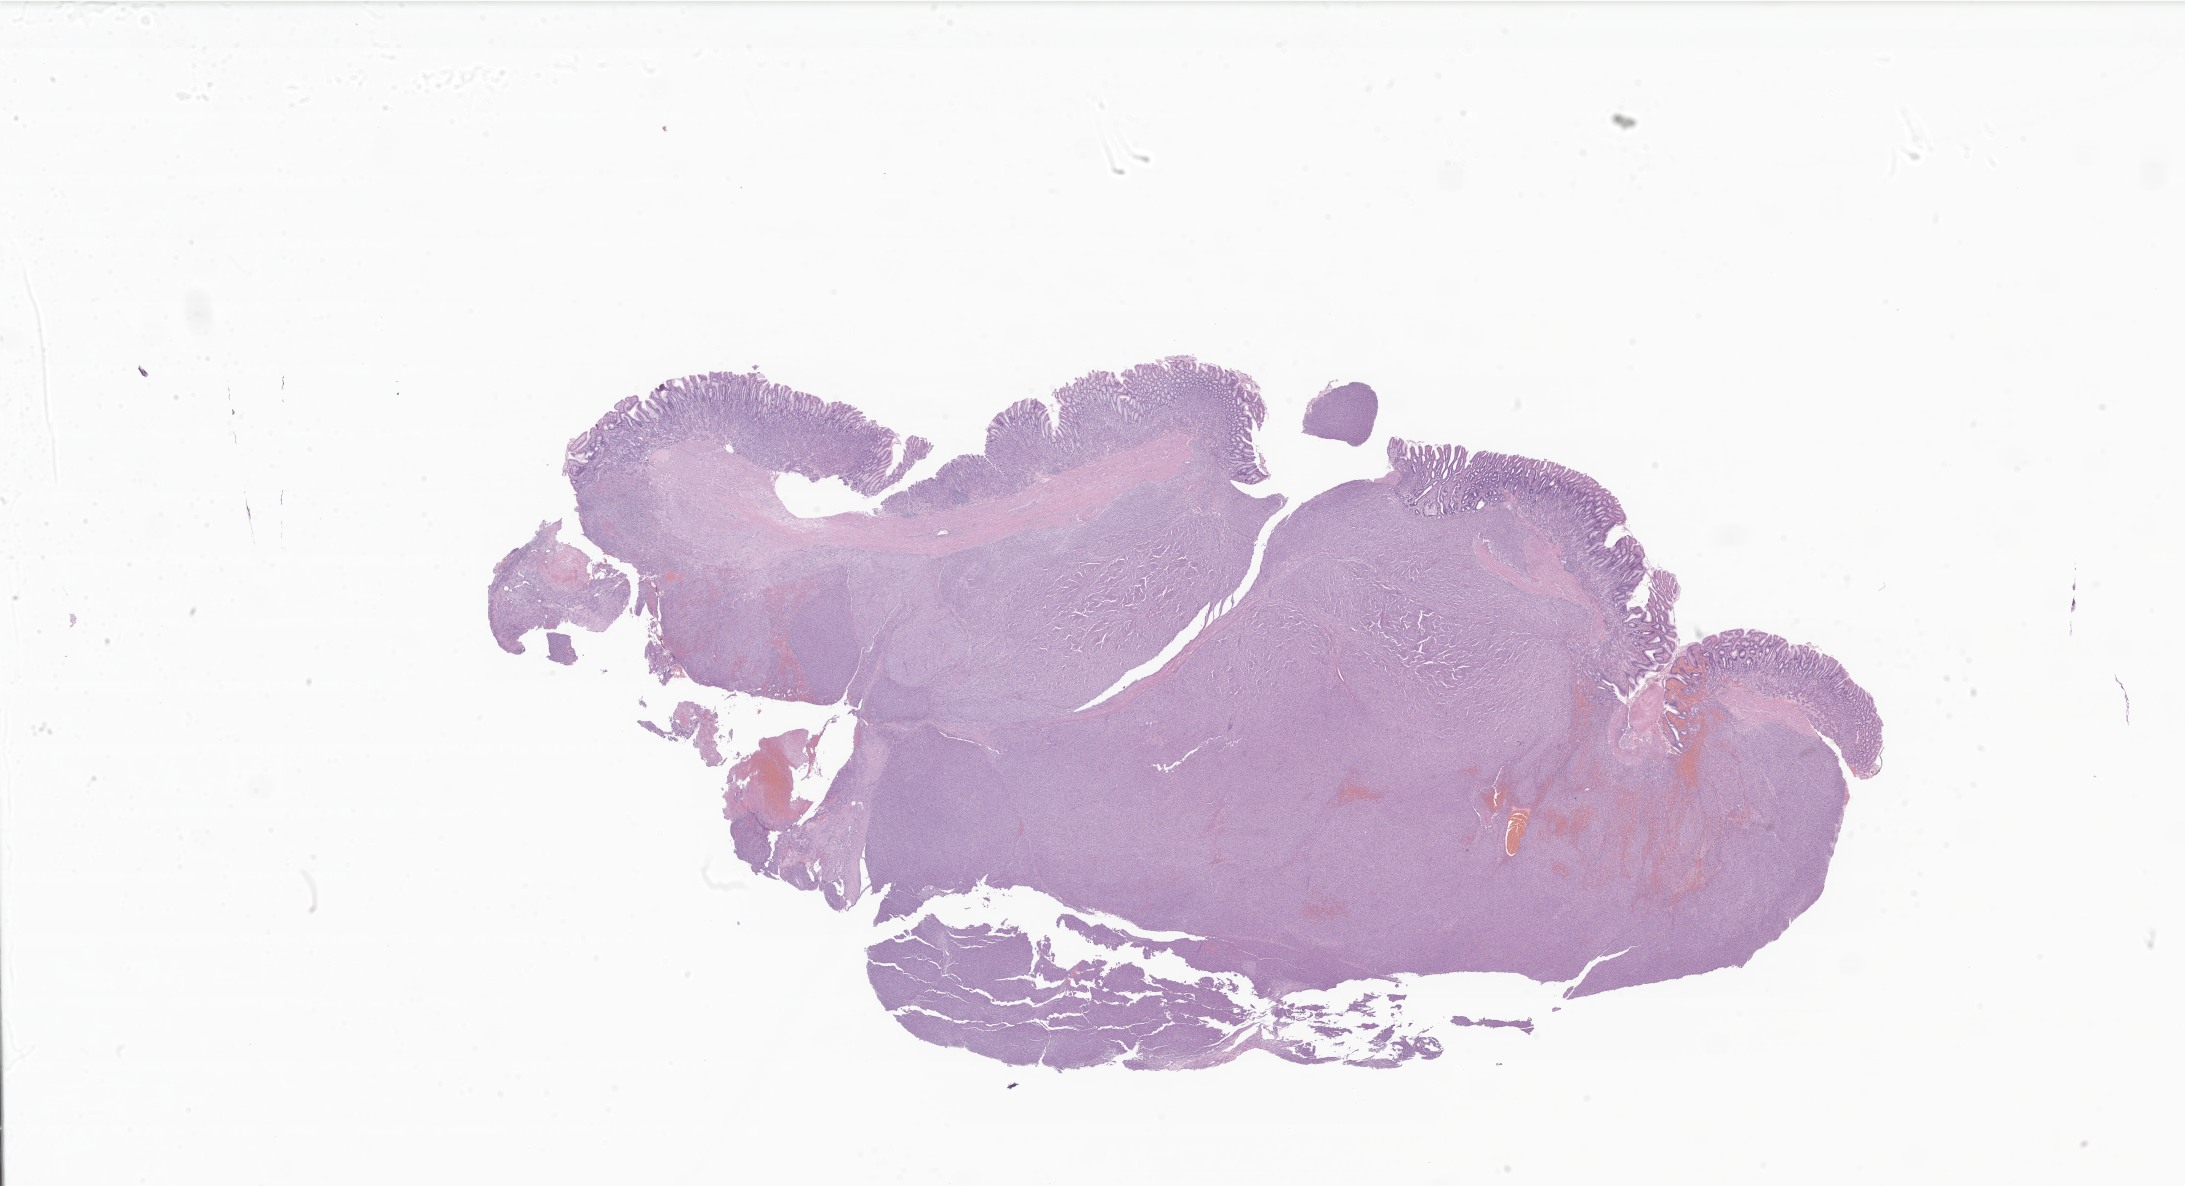
Digitized haematoxylin and eosin-stained section of tumor tissue from the stomach, shown as a low-resolution overview of the whole scanned area (about 36.9 x 20.0 mm). Formalin-fixed paraffin-embedded section. Patient male; age 283 months.
Diagnosis (ICD-O-3 morphology term): Gastrointestinal stromal tumor, NOS.